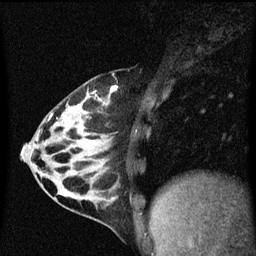
Breast MRI (dynamic contrast-enhanced), one sagittal slice. Slice 24 of 60 in the series (ordered by position). Dynamic contrast-enhanced series, image 2 of 3 at this slice position (ordered by acquisition). 1.5 T. TE 4.2 ms, TR 8.4 ms. 2 mm slice thickness. 256 × 256 image matrix, field of view 200 × 200 mm. Patient: female, 32 years.
Annotated regions visible in this slice (semi-automatically segmented with operator editing):
- analysis volume of interest (the breast-tissue region the enhancement analysis was run in; not a lesion): box from (x=34, y=74) to (x=149, y=169) px
- tumour enhancement mask (voxels above the 70 % enhancement threshold inside the analysis volume of interest): (x=49, y=86)–(x=119, y=121)